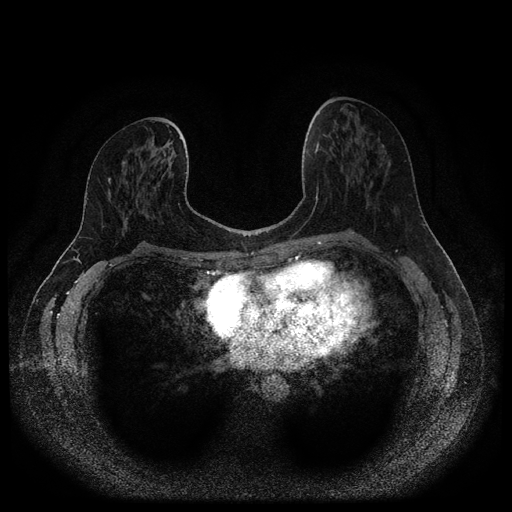
Breast MRI (dynamic contrast-enhanced, multi-phase), one axial slice; position 49 of 116 along the scan axis; dynamic contrast-enhanced series, time point 2 of 5 at this slice position (early post-contrast); 1.5 T; TE 2.7 ms, TR 5.4 ms; 2 mm slice thickness; 512 × 512 image matrix. Female patient, age 46 years.
Structures marked on this image (semi-automatic segmentation, software-assisted and operator-edited):
- breast lesion (labelled benign in the annotation): box from (x=122, y=162) to (x=126, y=166) px